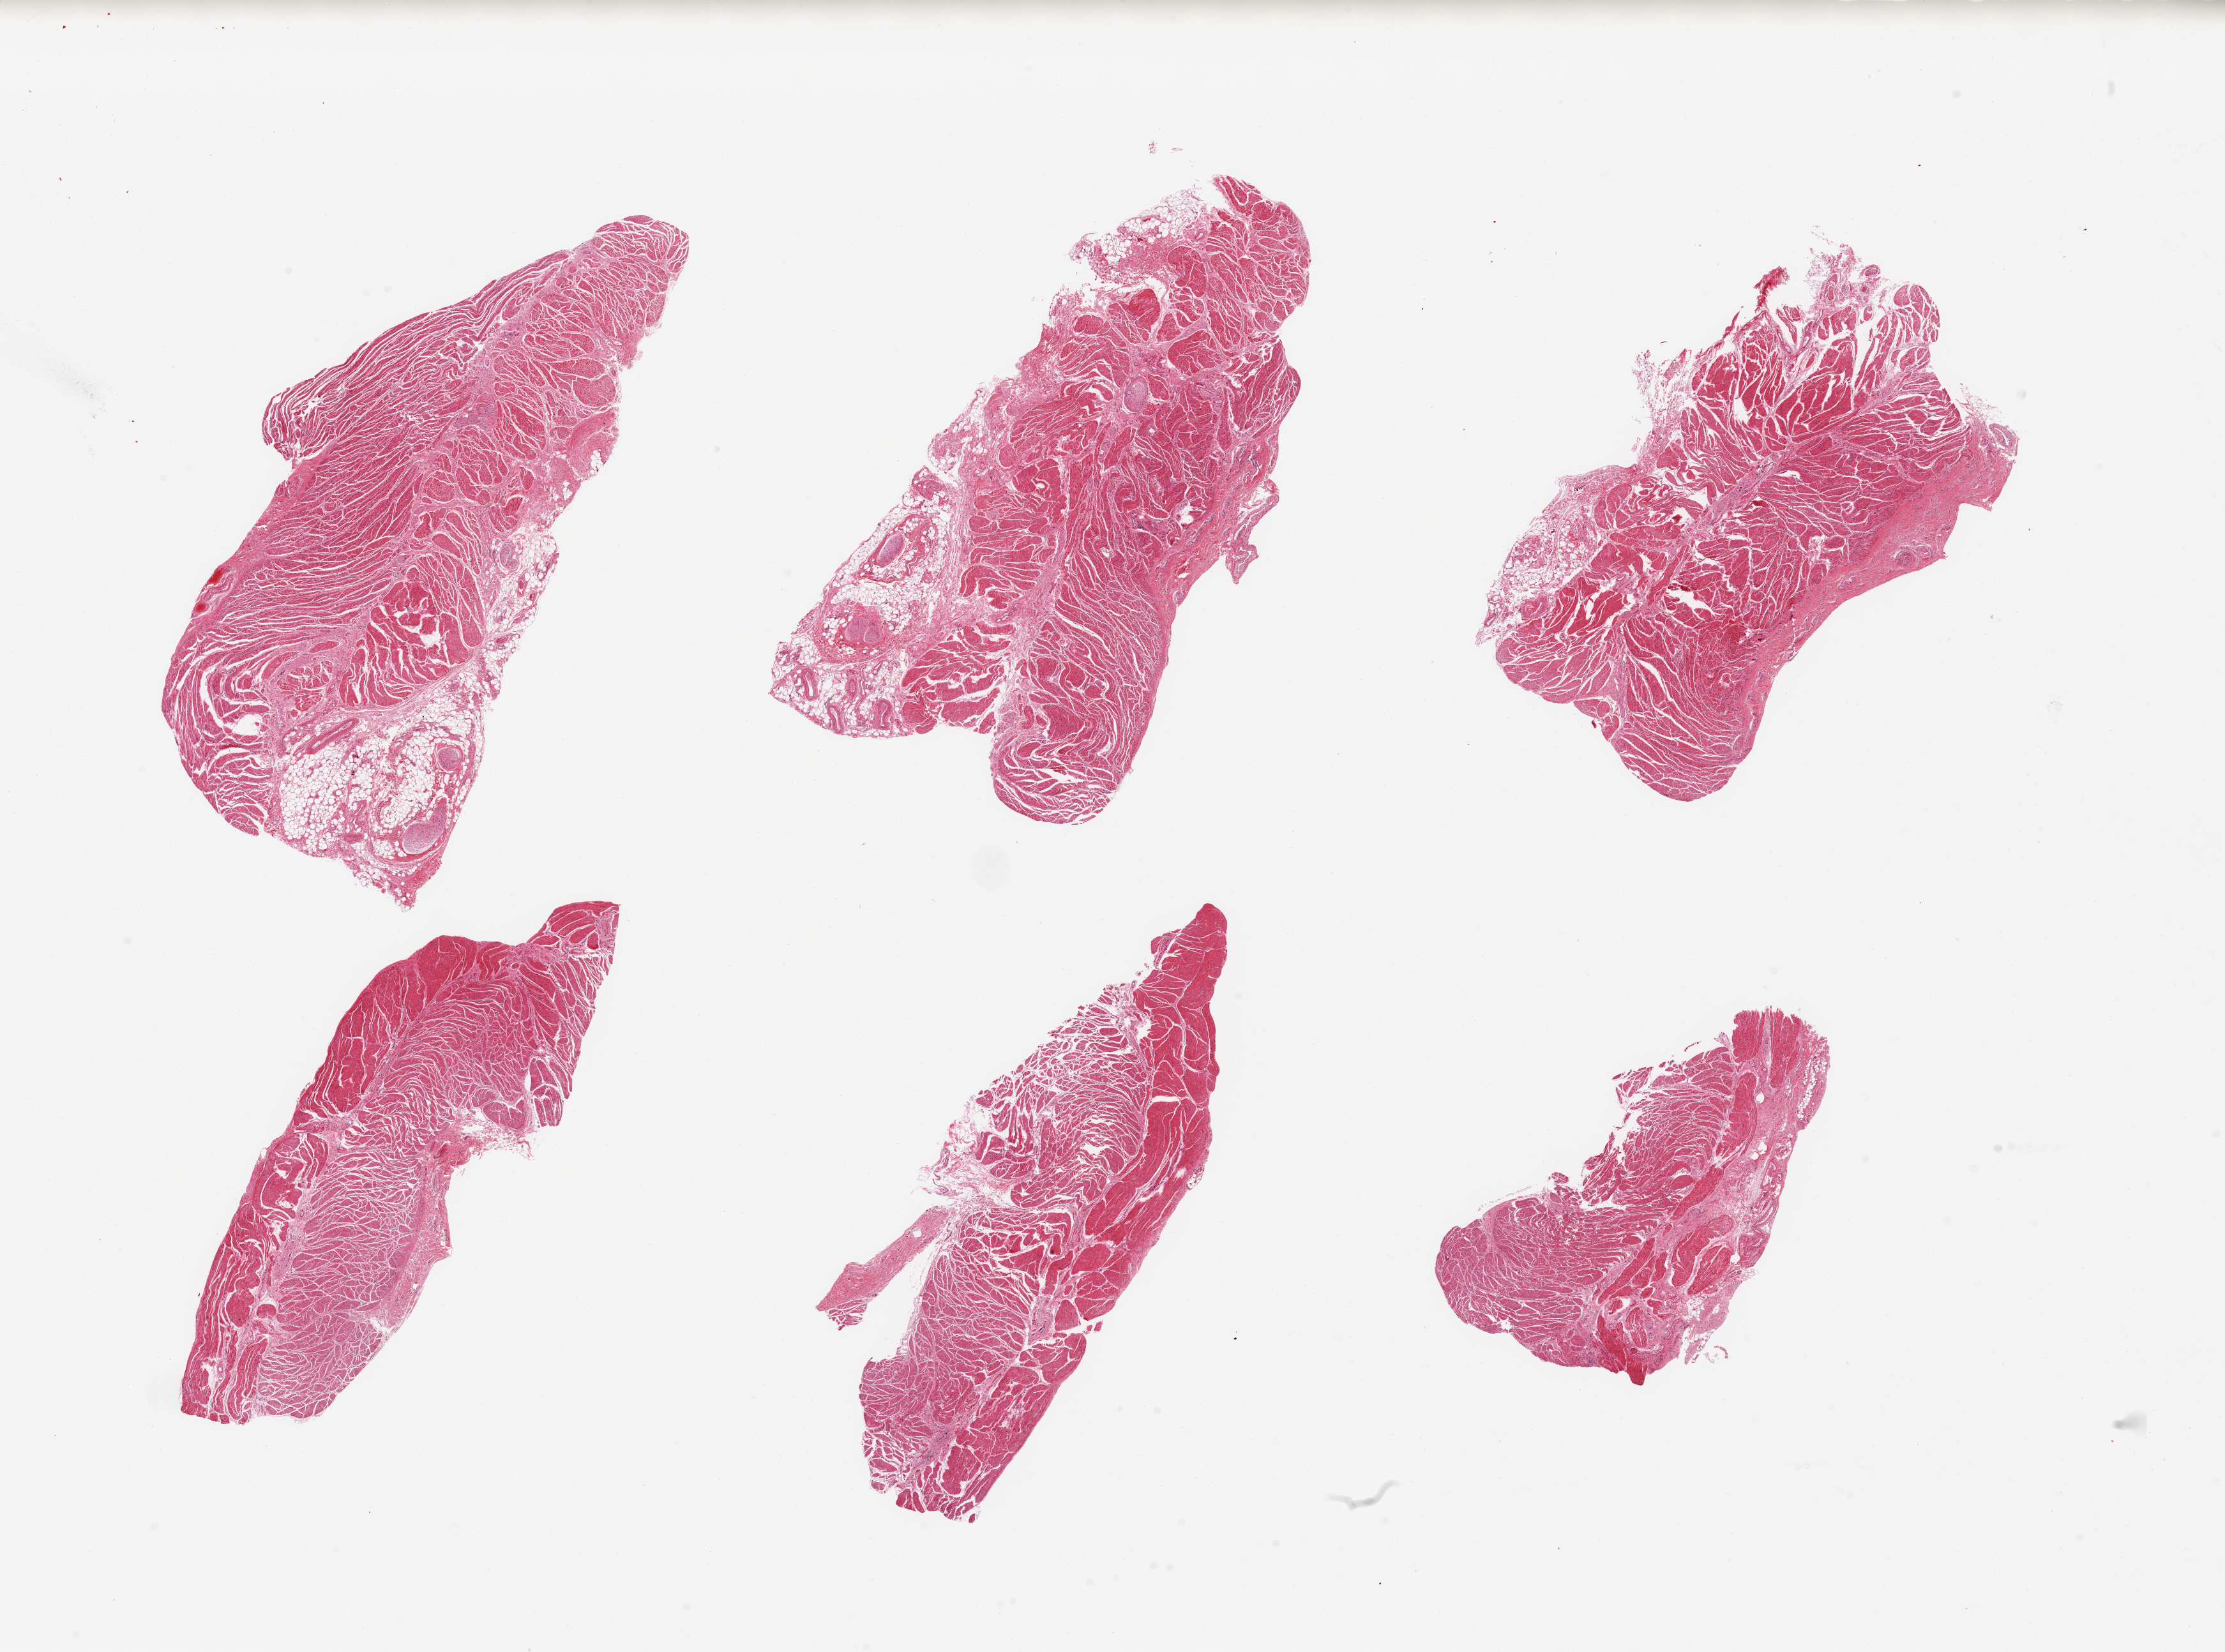
Hematoxylin and eosin (H&E) whole-slide image, brightfield — shown as a low-resolution overview of the whole scanned area (about 27.6 x 20.5 mm); PAXgene-fixed paraffin-embedded (PFPE) section; sampled site (target tissue): gastroesophageal junction; tissue donor sample. Male donor.
Reviewer comment on this tissue sample: 6 pieces, confirmed target muscularis.